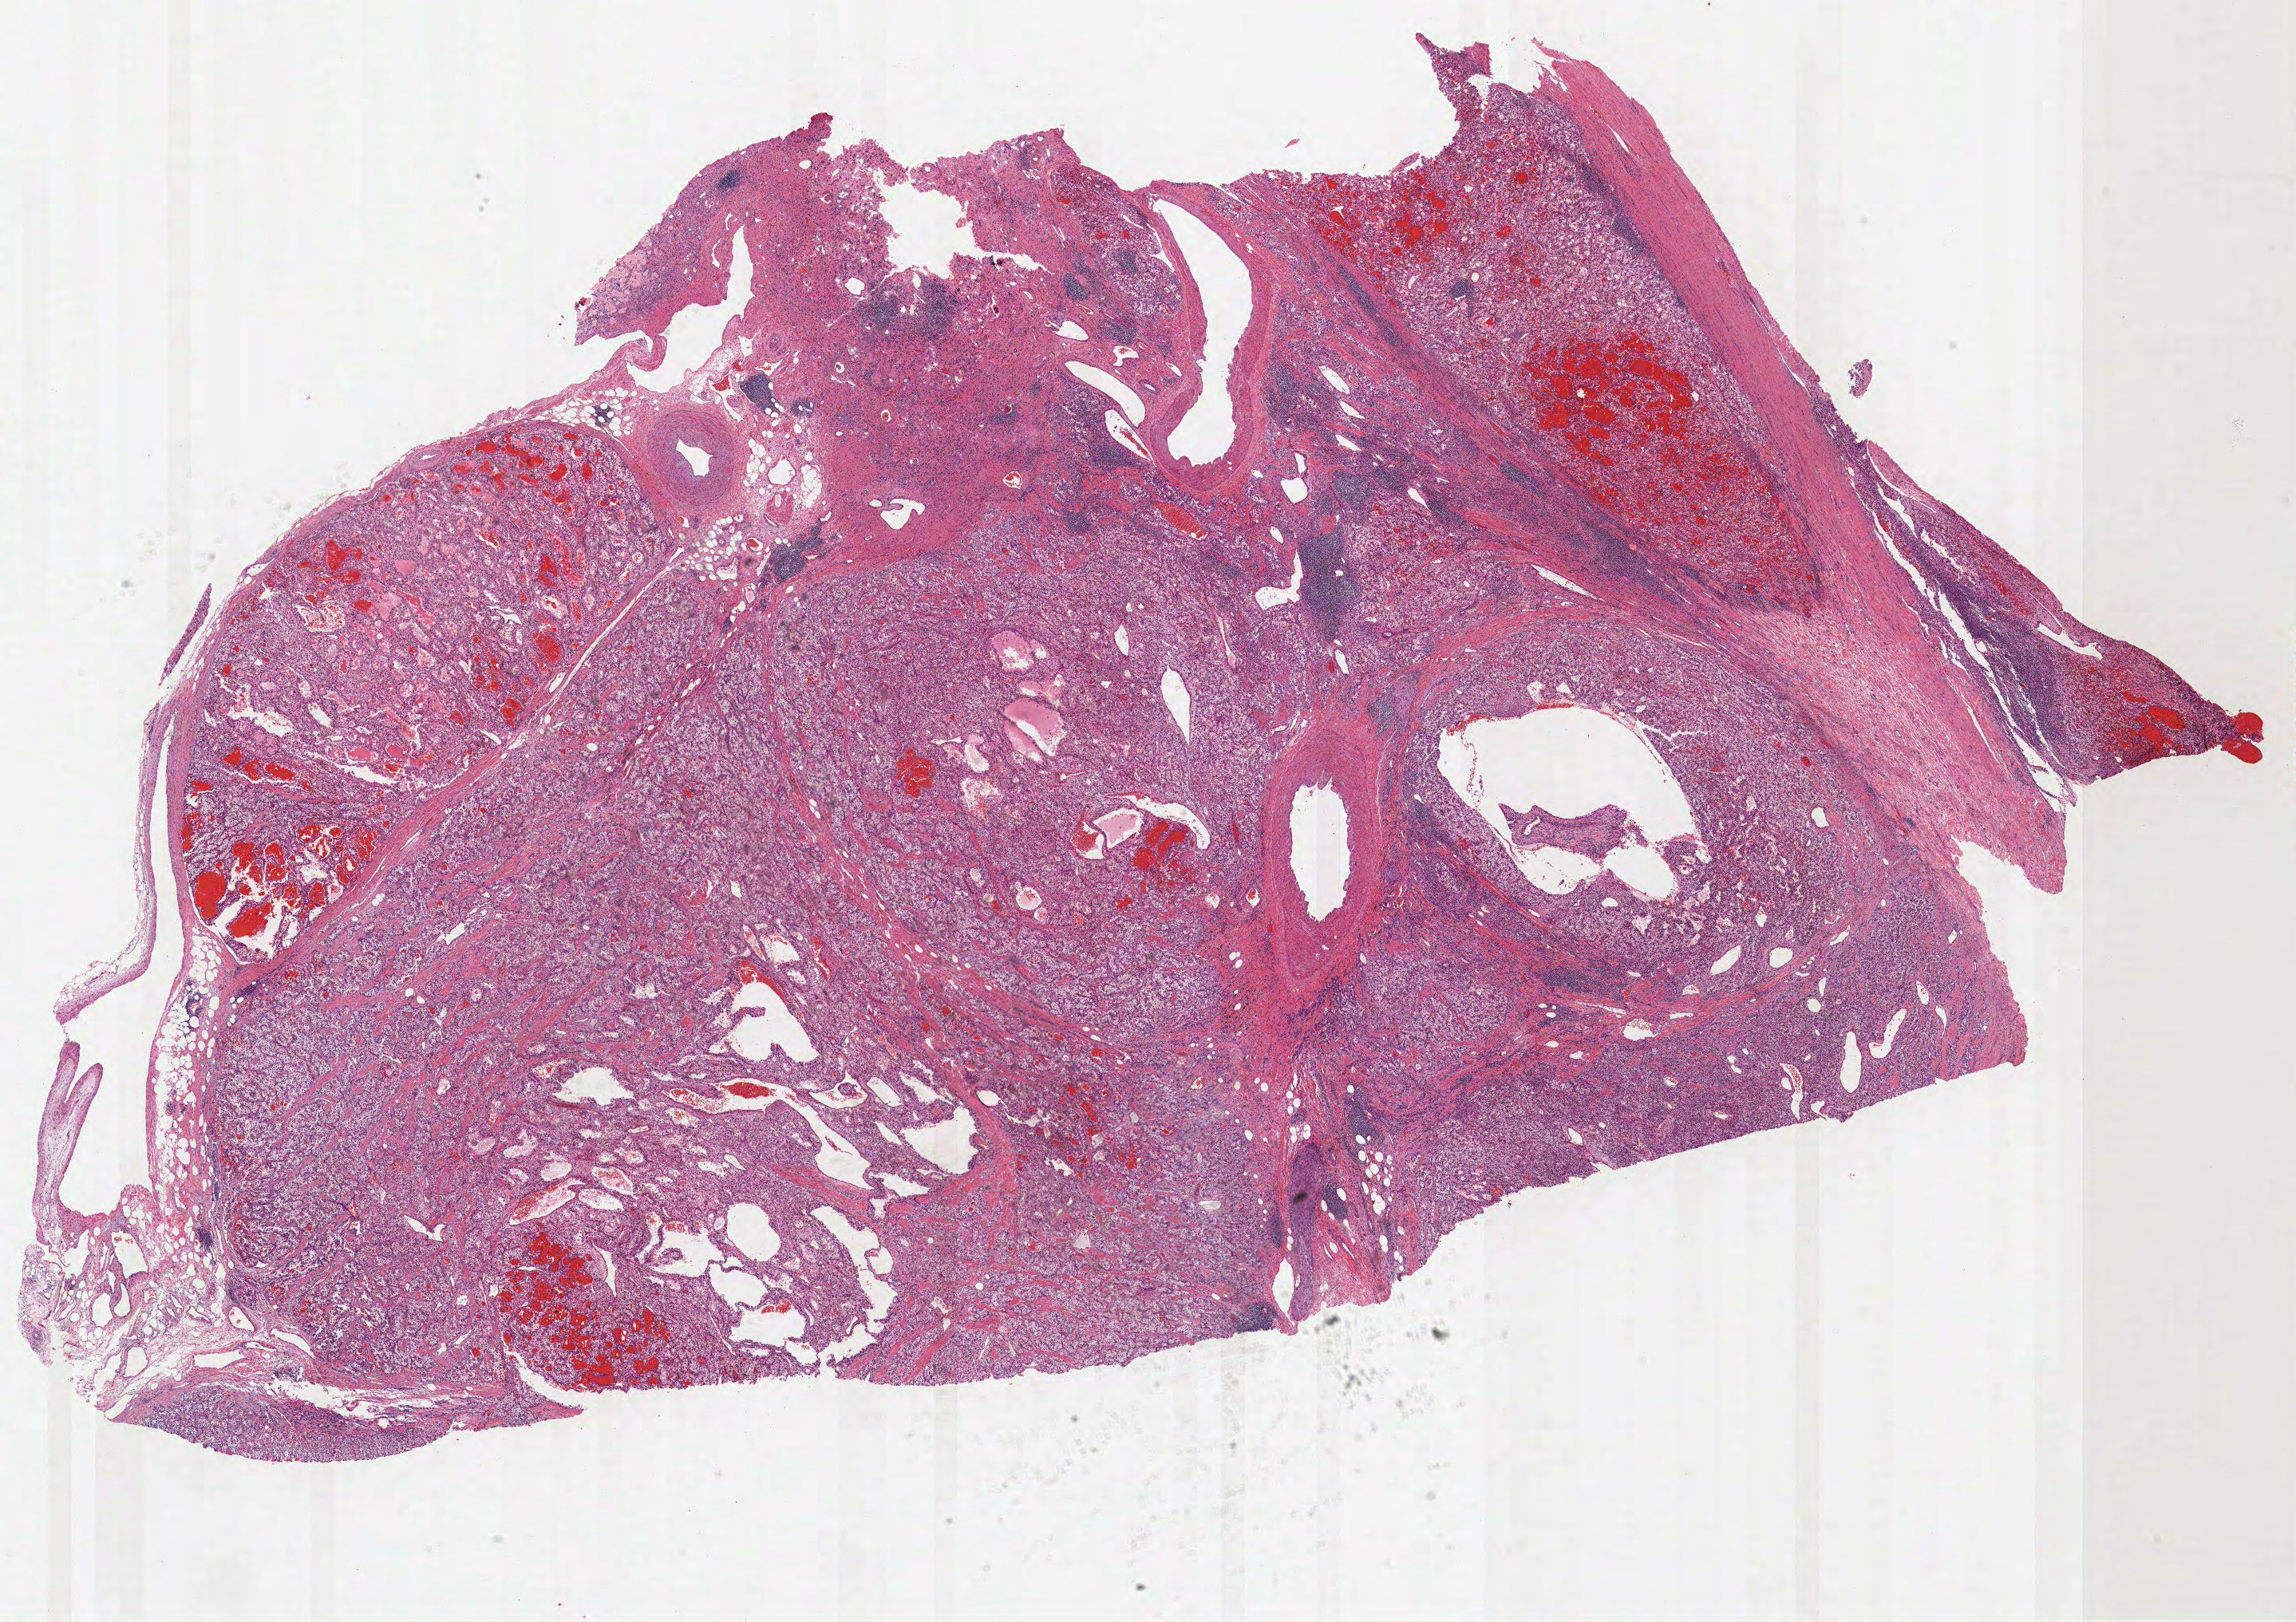
Whole-slide histology image, Hematoxylin and eosin (H&E) stained, a low-resolution overview of the entire scanned area, about 23.2 x 16.4 mm (acquisition: 40x scan); formalin-fixed paraffin-embedded (FFPE) diagnostic section; sample: primary tumour, kidney. Male, age 81 years at initial diagnosis.
Pathologic diagnosis: Clear cell adenocarcinoma, NOS.